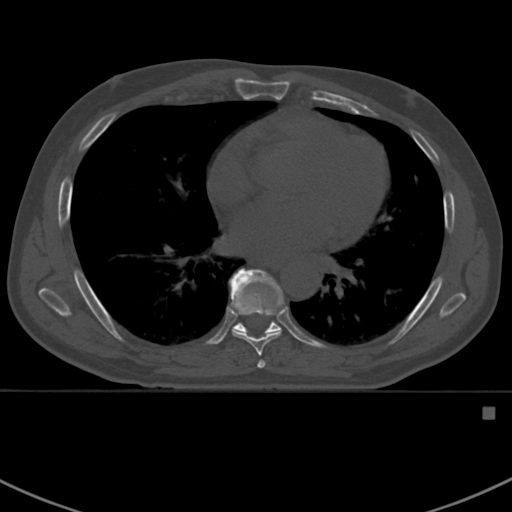
CT including the spine, one axial slice; slice 411 of 412 in the series (ordered by position); reconstruction kernel Br40s; bone window (W 1800 / L 400 HU); 512 × 512 image matrix. Patient: male, 59 years. From the clinical record (not read from this slice): primary cancer: prostate.
Structures marked on this image (semi-automatic segmentation, software-assisted and operator-edited):
- T7 vertebra: bounding box (x1, y1, x2, y2) in pixels: (229, 268, 284, 369)
- T8 vertebra: (231, 267, 282, 335)